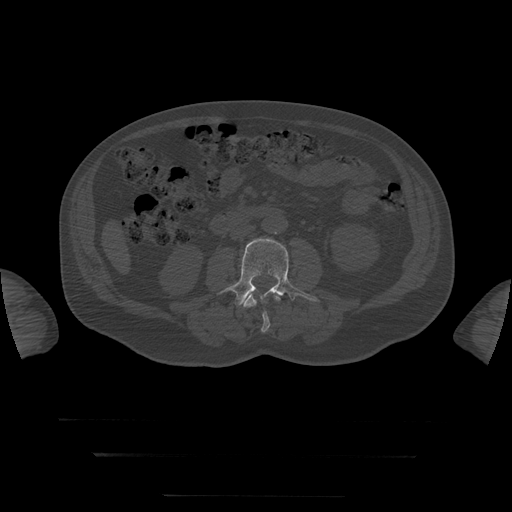
CT including the spine, one axial slice. Position 2 of 397 along the scan axis. 120 kVp. Bone window (W 1800 / L 400 HU). 1.25 mm slice thickness. 512 × 512 image matrix. Patient age 73 years. From the clinical record (not read from this slice): primary cancer: prostate.
Structures marked on this image (semi-automatic segmentation, software-assisted and operator-edited):
- L3 vertebra: bounding box [x1, y1, x2, y2] px = [221, 238, 320, 306]